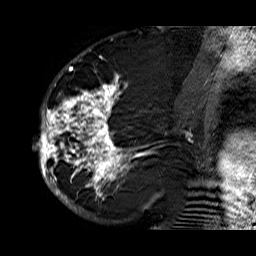
Breast MRI (dynamic contrast-enhanced), one sagittal slice; slice 32 of 60 in the series (ordered by position); dynamic contrast-enhanced series, time point 2 of 6 at this slice position (early post-contrast); 1.5 T; TE 6.3 ms, TR 32.9 ms; 256 × 256 image matrix, field of view 200 × 200 mm. Female patient. From the clinical record (not read from this slice): setting: breast cancer imaged before/during neoadjuvant chemotherapy; receptor status: HR-positive, HER2-negative.
Annotated regions visible in this slice (semi-automatic segmentation, software-assisted and operator-edited):
- analysis volume of interest (the breast-tissue region the enhancement analysis was run in; not a lesion): bounding box [x1, y1, x2, y2] px = [33, 74, 176, 210]
- tumour enhancement mask (voxels above the 100 % enhancement threshold inside the analysis volume of interest): [33, 76, 152, 210]